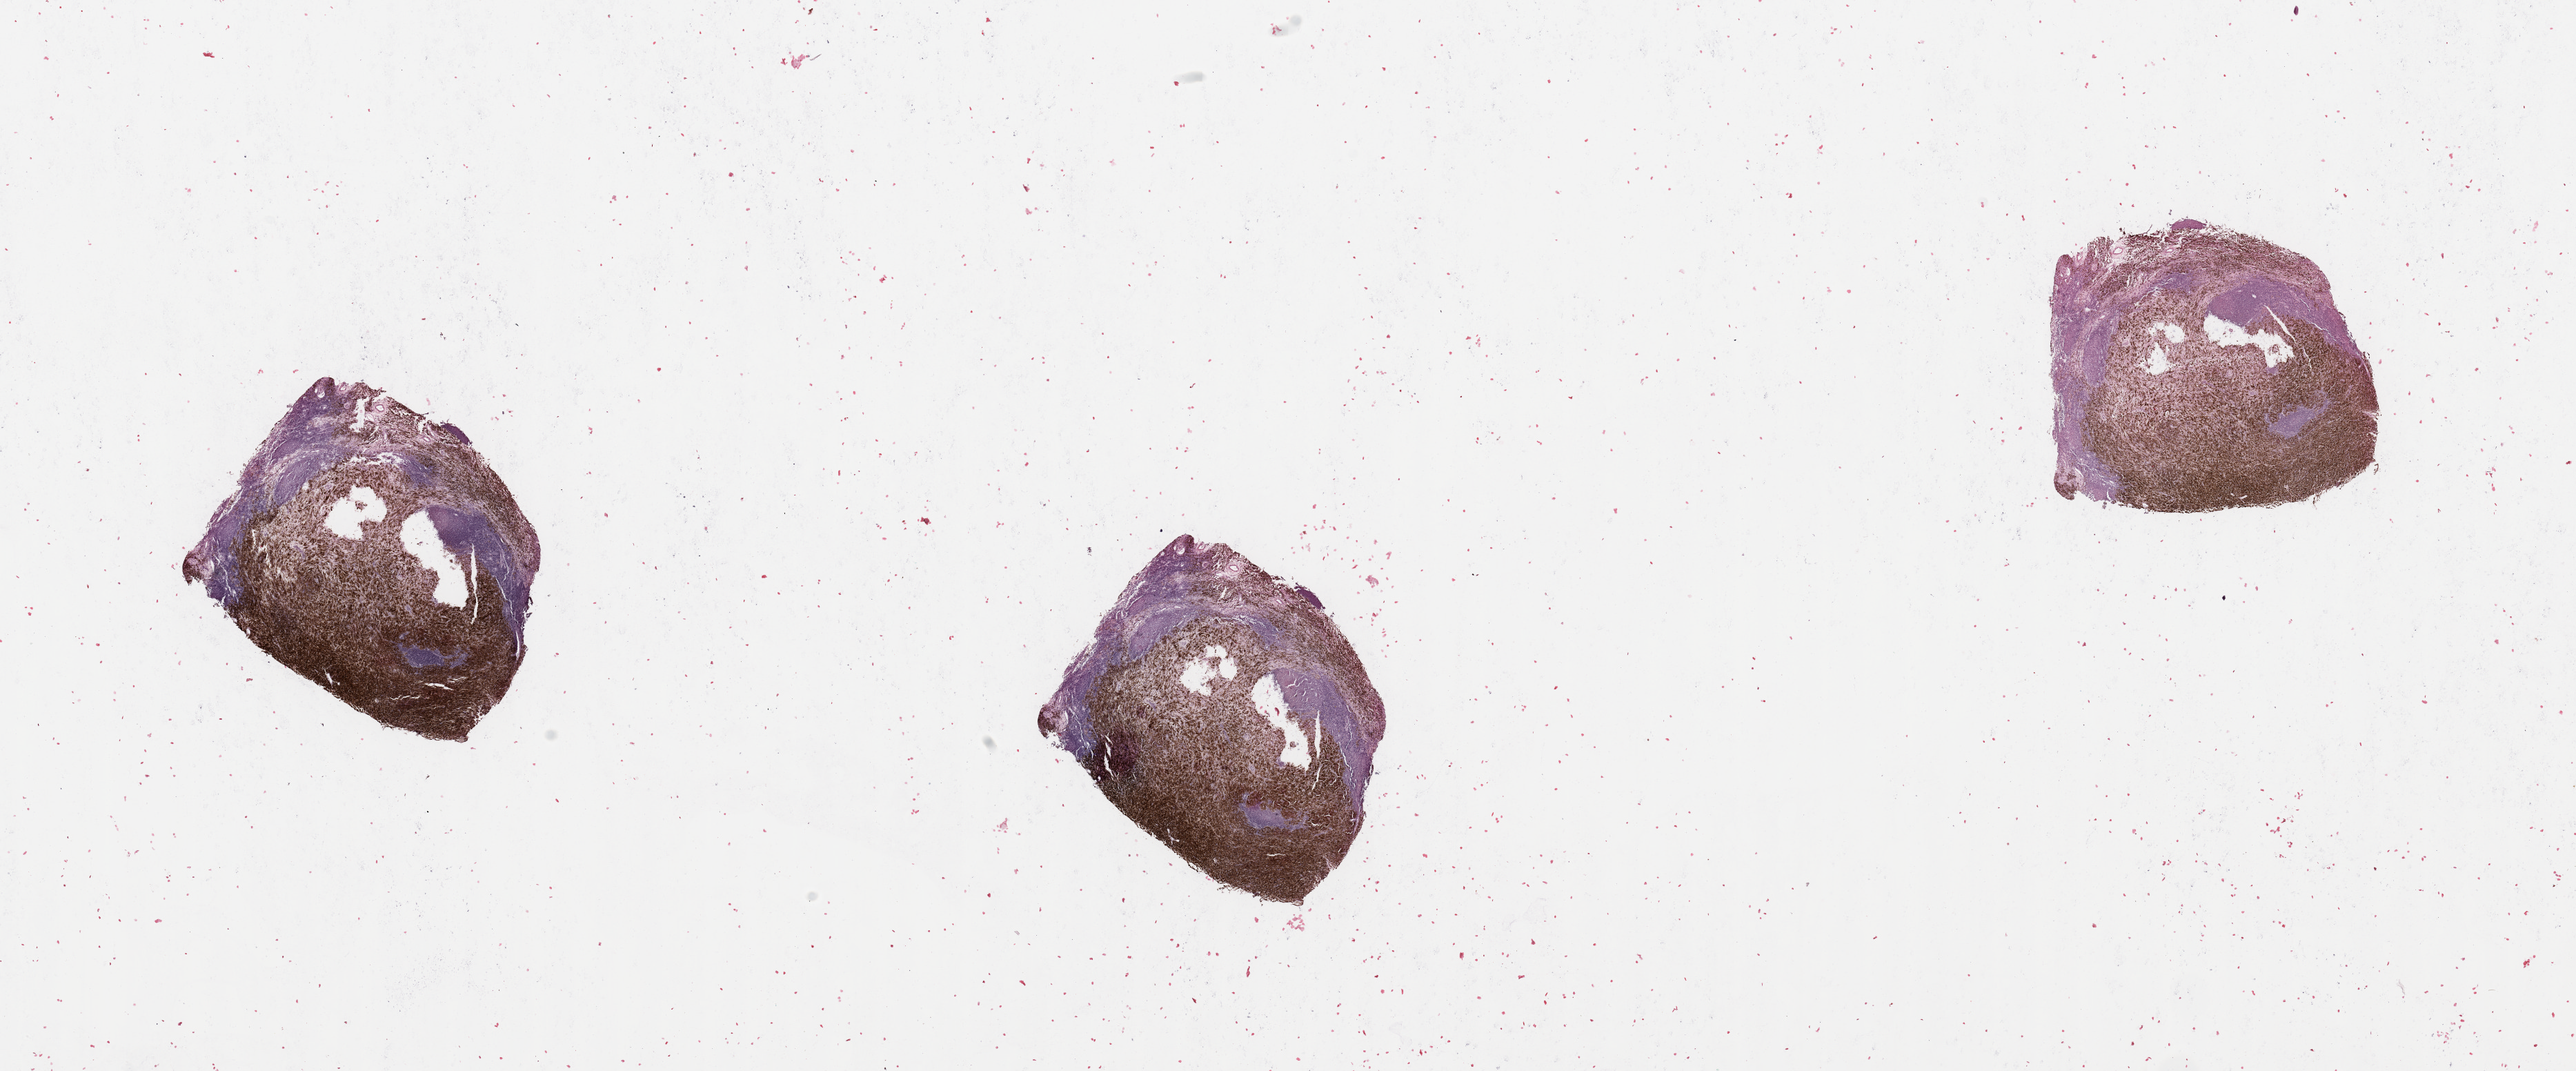
Digitized Hematoxylin and eosin (H&E) stained tissue section (whole slide), whole scanned area (about 29.5 x 12.3 mm) shown as a low-resolution overview. Tumour tissue sample, sampled site: lymph node. Patient: male, age 59 years.
Patient diagnosis (cohort enrolment): cutaneous melanoma (skin).